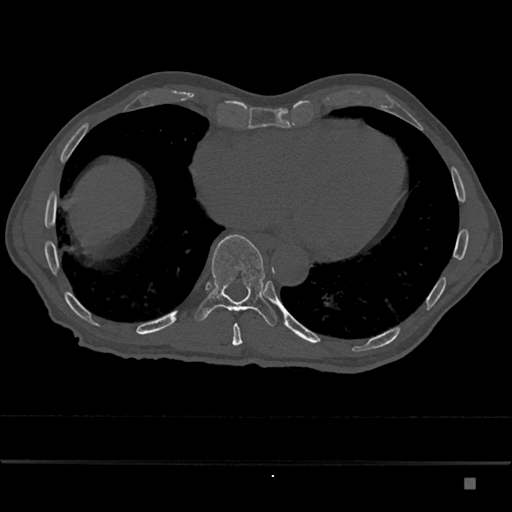
CT including the spine, one axial slice; position 754 of 797 along the scan axis; reconstruction kernel Br40s/3; 120 kVp; bone window (W 1800 / L 400 HU); 0.5 mm slice thickness; 512 × 512 image matrix, field of view 390 × 390 mm. Patient: male, 72 years. Case-level facts recorded for this patient, not image findings: primary cancer: prostate.
Outlined on this slice (semi-automatic segmentation, software-assisted and operator-edited):
- T10 vertebra: box from (x=194, y=234) to (x=277, y=327) px
- T9 vertebra: (x=232, y=323)–(x=242, y=346)